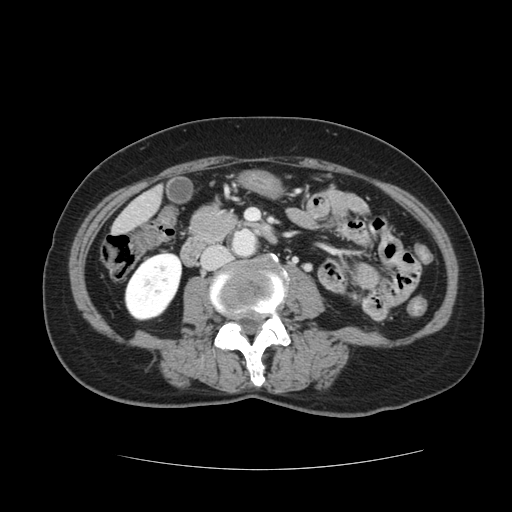
Contrast-enhanced abdominal CT, one axial slice. Position 17 of 128 along the scan axis. Intravenous contrast given. Soft-tissue window (W 400 / L 40 HU). 2.5 mm slice thickness. 512 × 512 image matrix, field of view 366 × 366 mm. Female patient, age 67 years. Case-level facts recorded for this patient, not image findings: diagnosis: colorectal cancer liver metastases, imaged before liver resection; multiple liver metastases: yes; largest metastasis: 3 cm.
Outlined on this slice (manually delineated by an expert):
- liver: bounding box <114,190,160,234> (left, top, right, bottom; pixels)
- planned liver remnant (the part of the liver to remain after resection): <114,206,144,235>